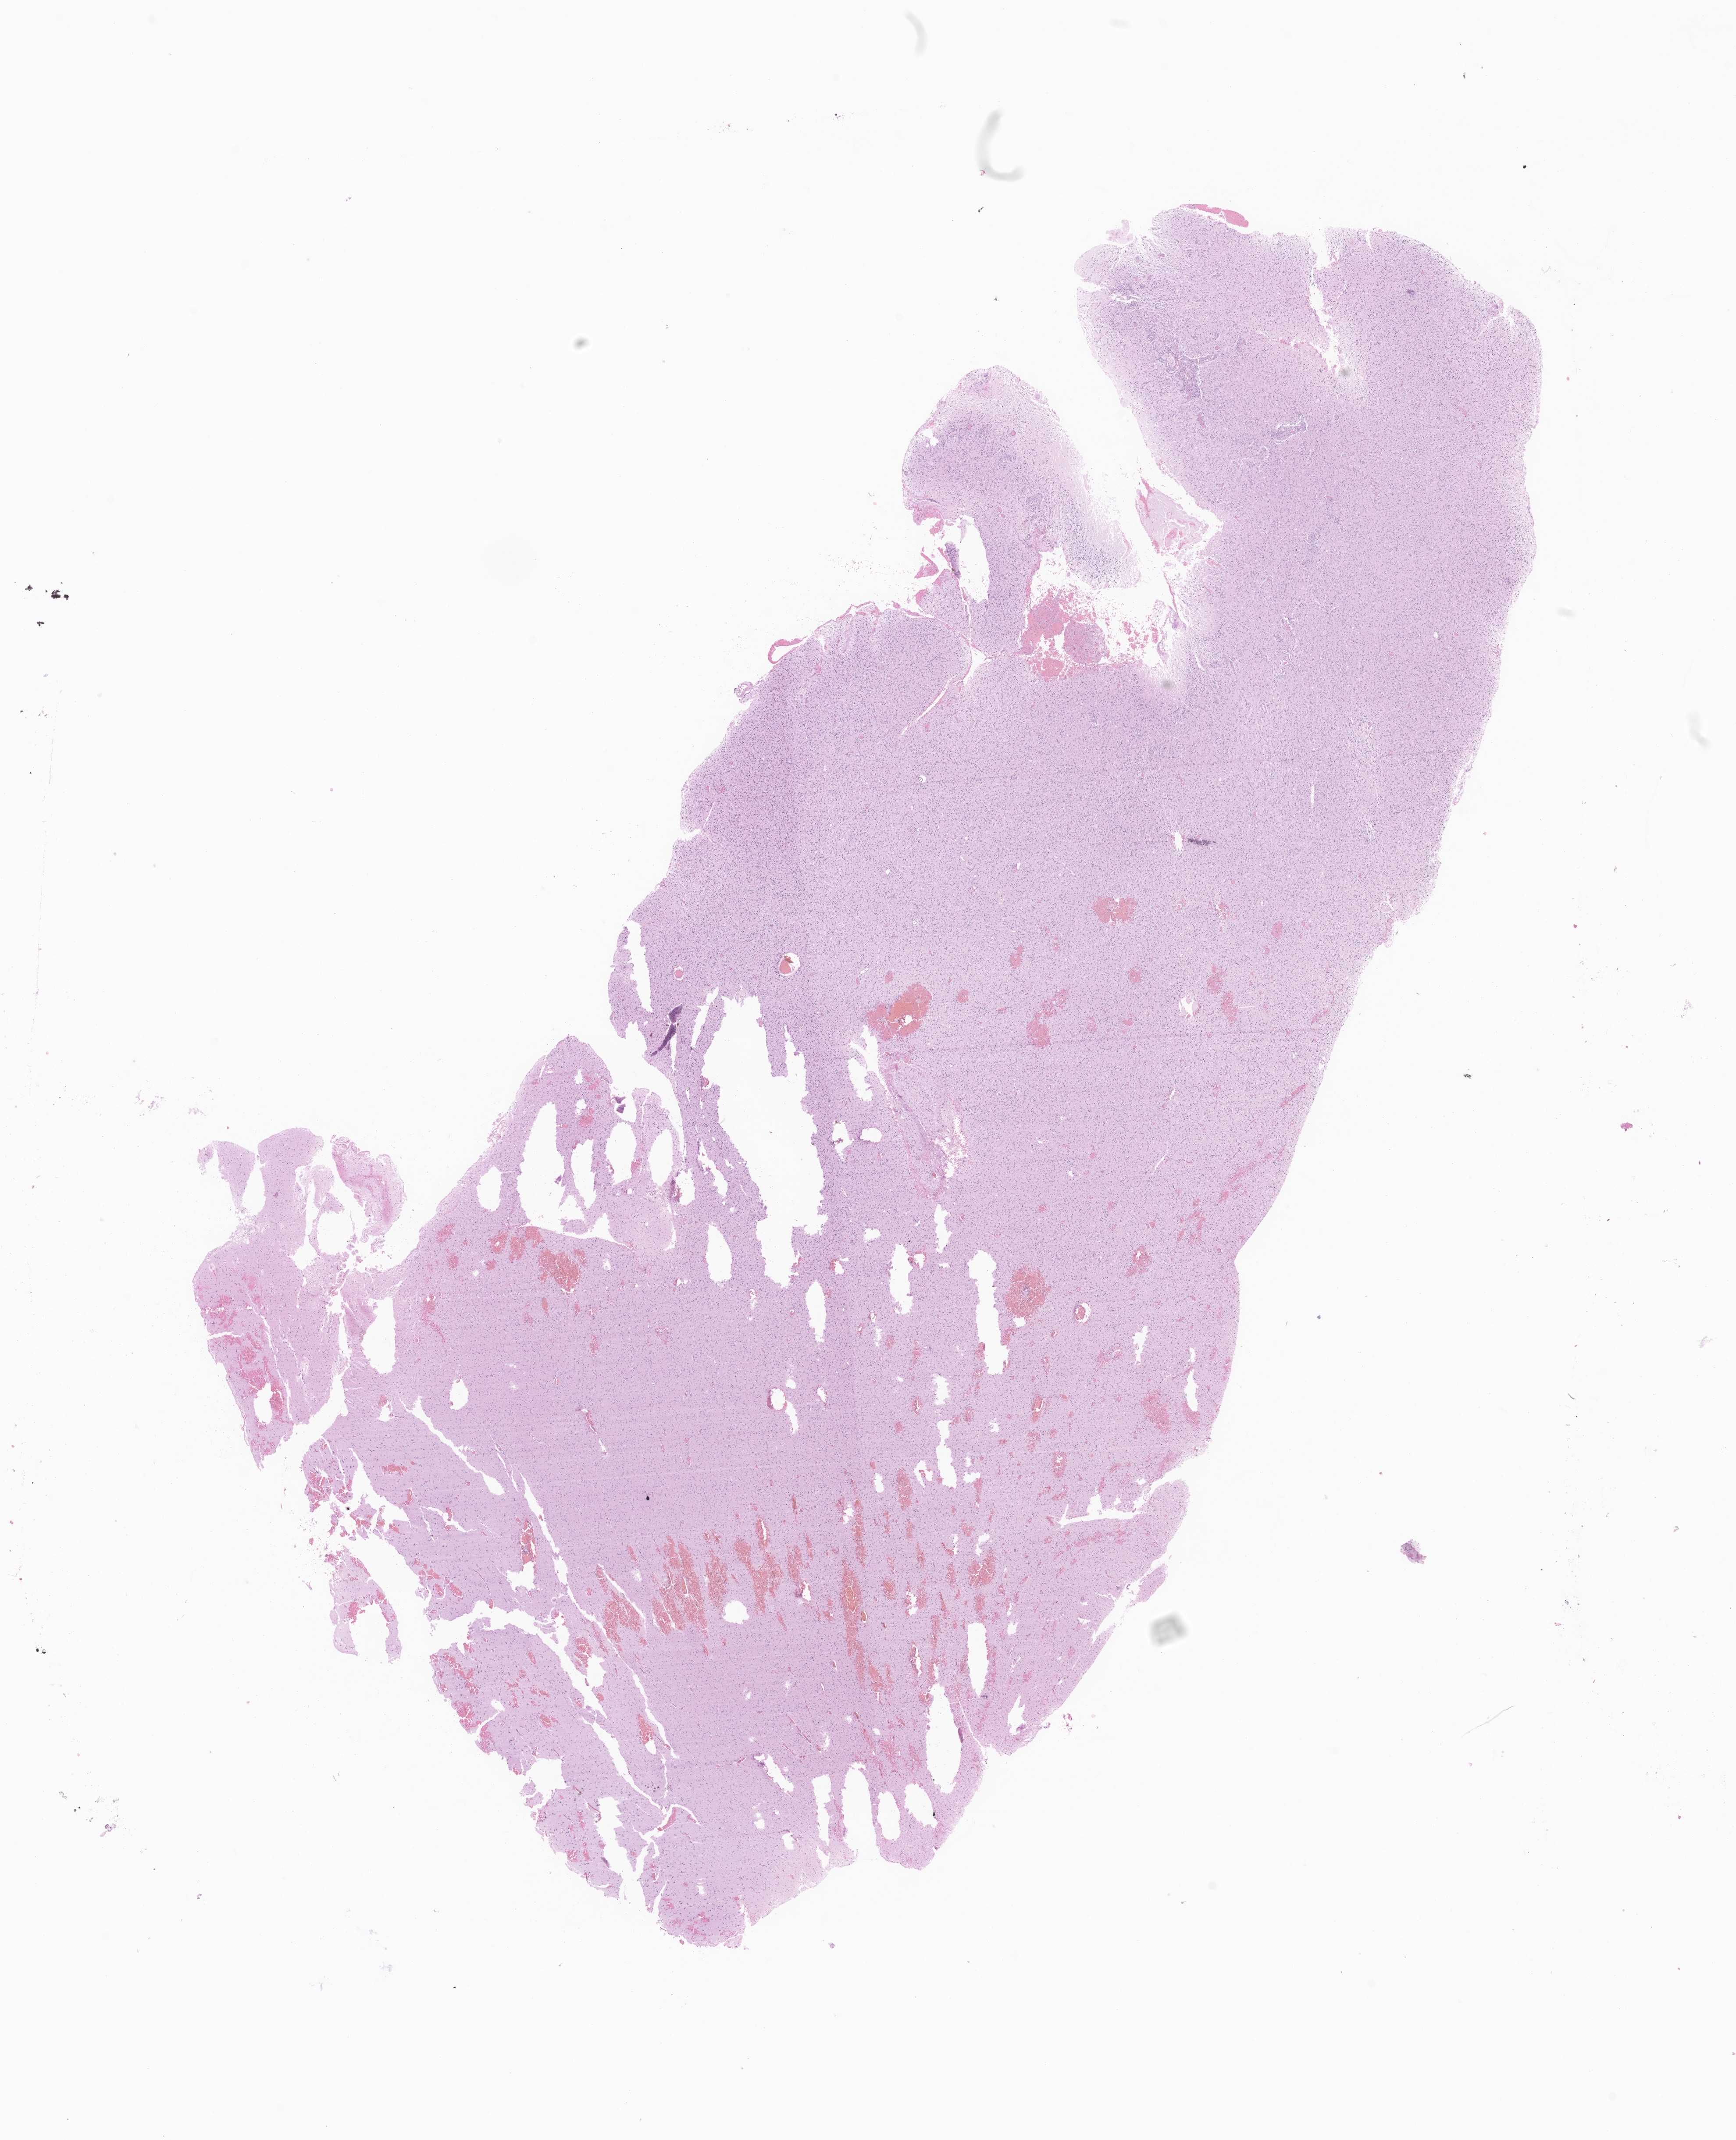
H&E whole-slide image of tumor tissue from the brain, a low-resolution overview of the entire scanned area, about 16.7 x 20.6 mm; formalin-fixed, paraffin-embedded (FFPE) tissue. Patient male; age 204 months.
* diagnosis (ICD-O-3 morphology term): Glioma, malignant